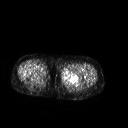
FDG PET of an extremity soft-tissue mass (from a PET/CT study), one axial slice; position 228 of 267 along the scan axis; 3.27 mm slice thickness; 128 × 128 image matrix. Patient: female, 42 years. Case-level facts recorded for this patient, not image findings: histological type: pleiomorphic leiomyosarcoma; grade: intermediate; site of the primary tumour: left thigh.
Structures marked on this image (expert contour drawn on MRI and transferred to this co-registered scan by the dataset authors):
- gross tumour volume including surrounding oedema: bounding box <61,68,82,81> (left, top, right, bottom; pixels)
- gross tumour volume (mass): <62,68,79,81>